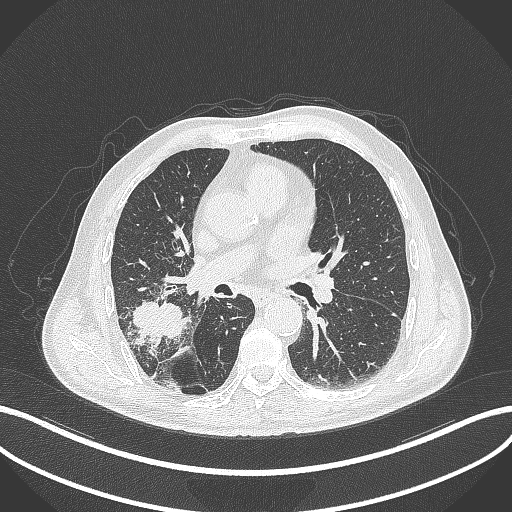
Chest CT, one axial slice. Slice 225 of 429 in the series (ordered by position). Reconstruction kernel B70f. Lung window (W 1500 / L -600 HU). 1 mm slice thickness. 512 × 512 image matrix, field of view 400 × 400 mm. Patient: male, 72 years. Case-level facts recorded for this patient, not image findings: clinical TNM (as recorded): T3 N2 M0.
Annotated regions visible in this slice (bounding box drawn by a radiologist):
- lung tumour (recorded histology: adenocarcinoma): bounding box [x1, y1, x2, y2] px = [127, 294, 187, 345]